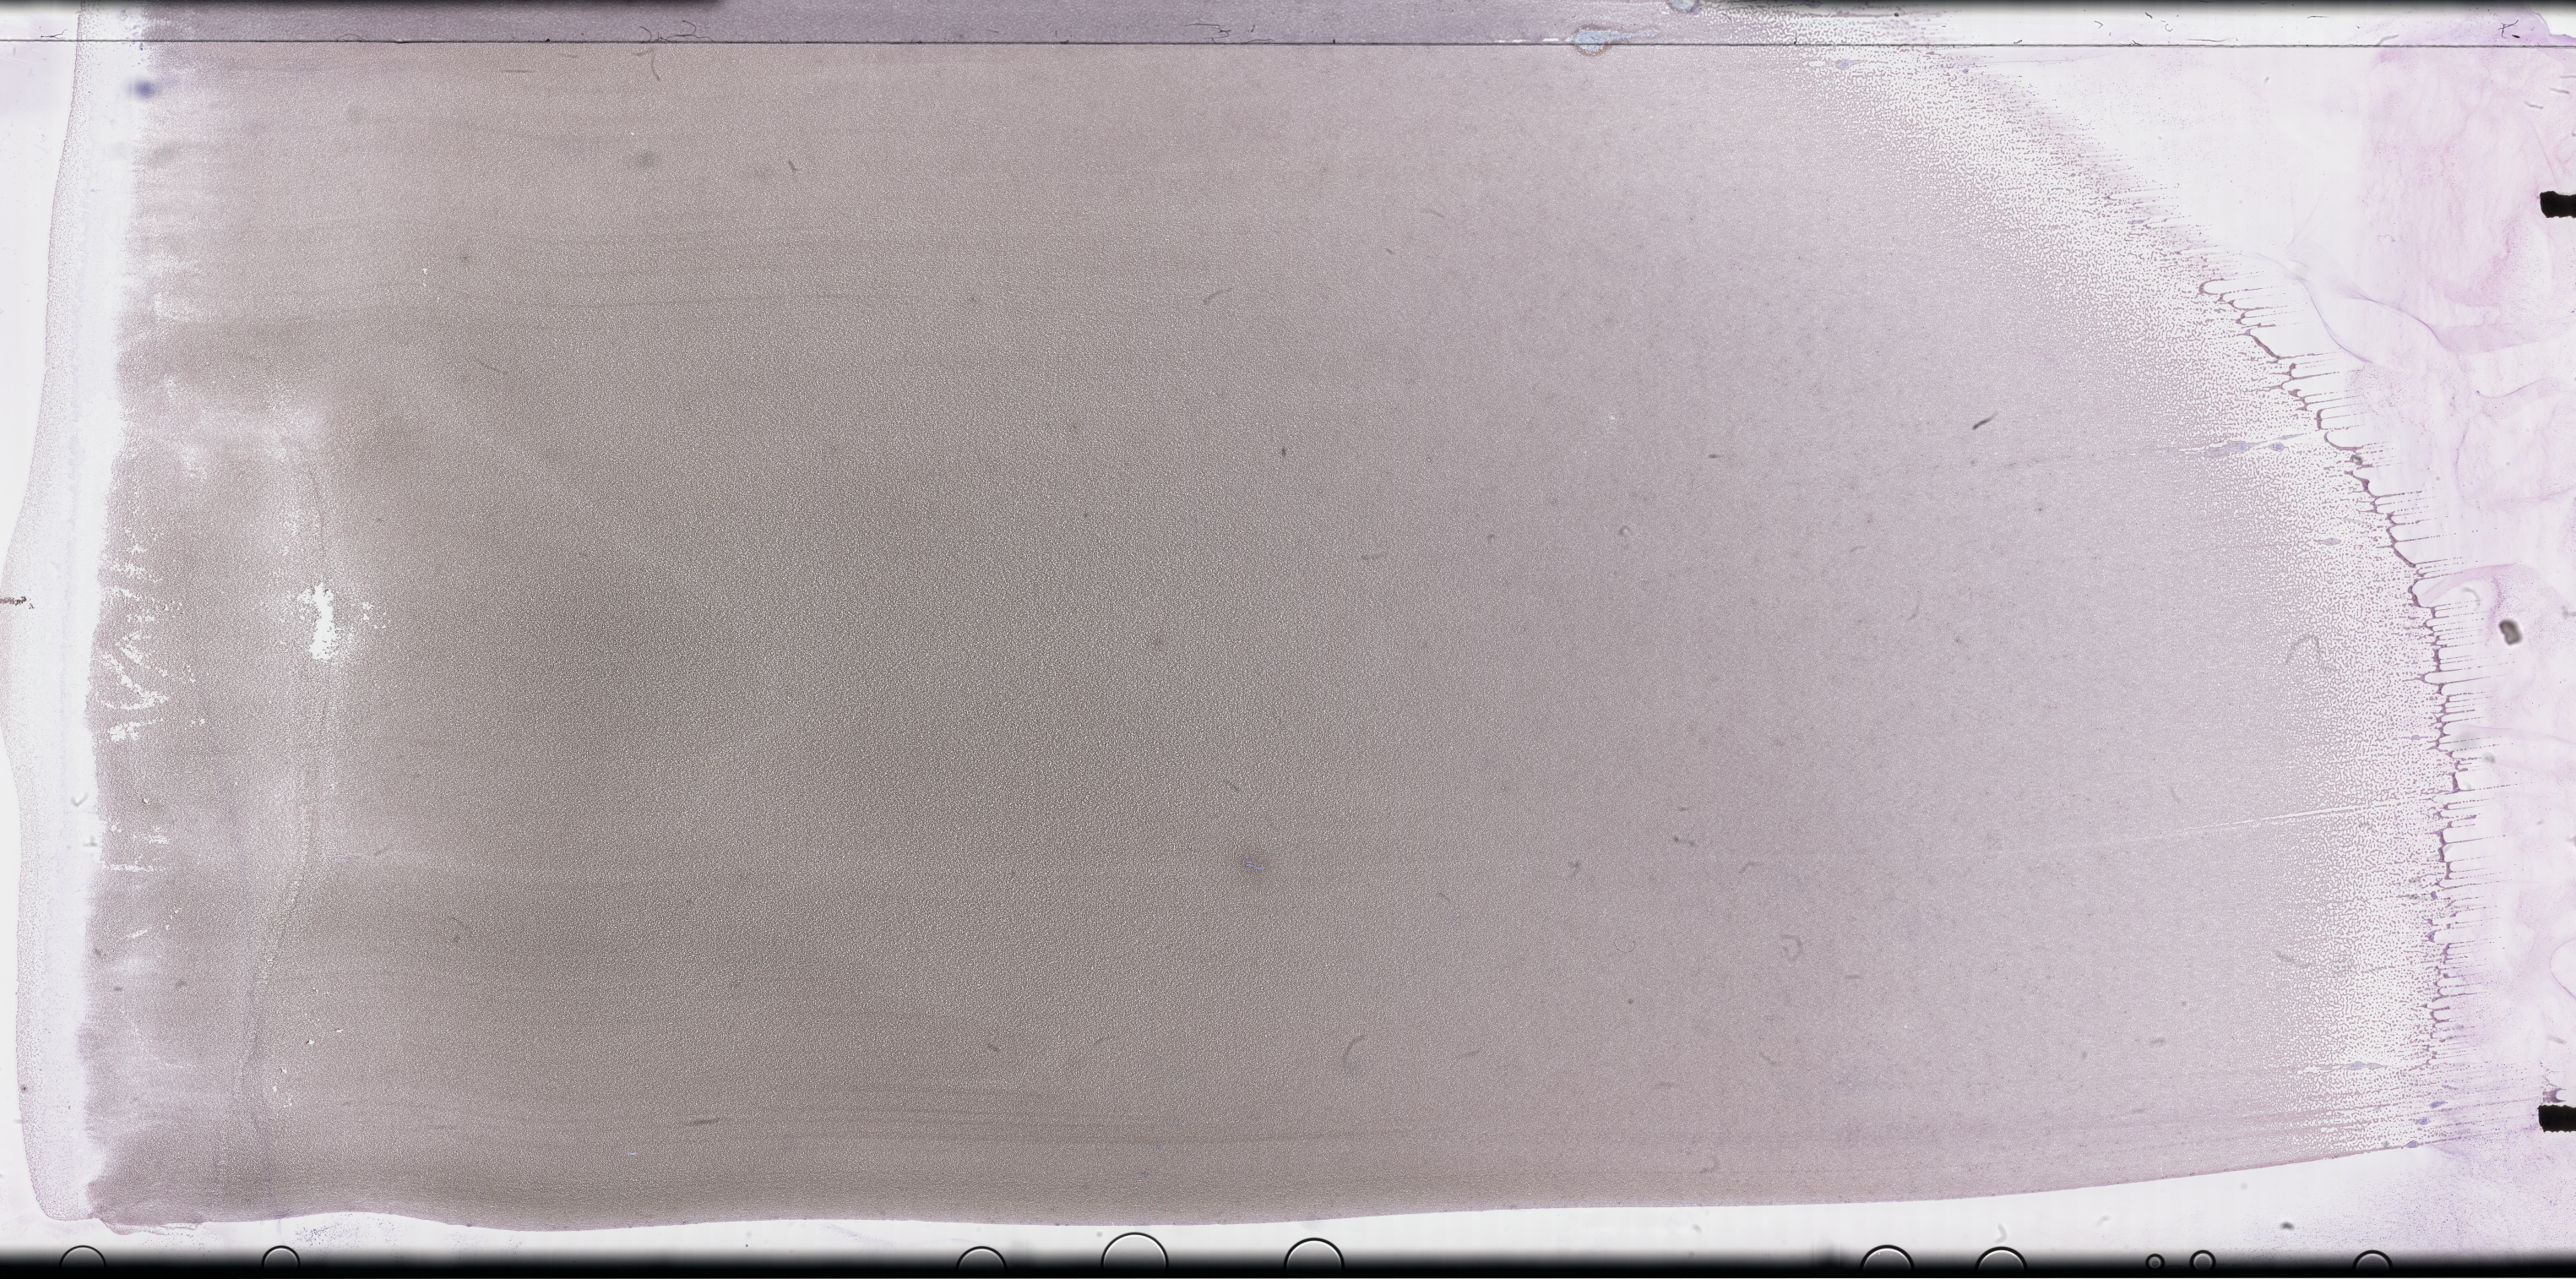
Whole-slide image of a whole blood smear, Wright–Giemsa stain, whole scanned area (about 49.3 x 24.4 mm) shown as a low-resolution overview, smear from an EDTA sample, specimen time point: collected on treatment. Patient sex: male.
Patient diagnosis: Plasma Cell Myeloma.